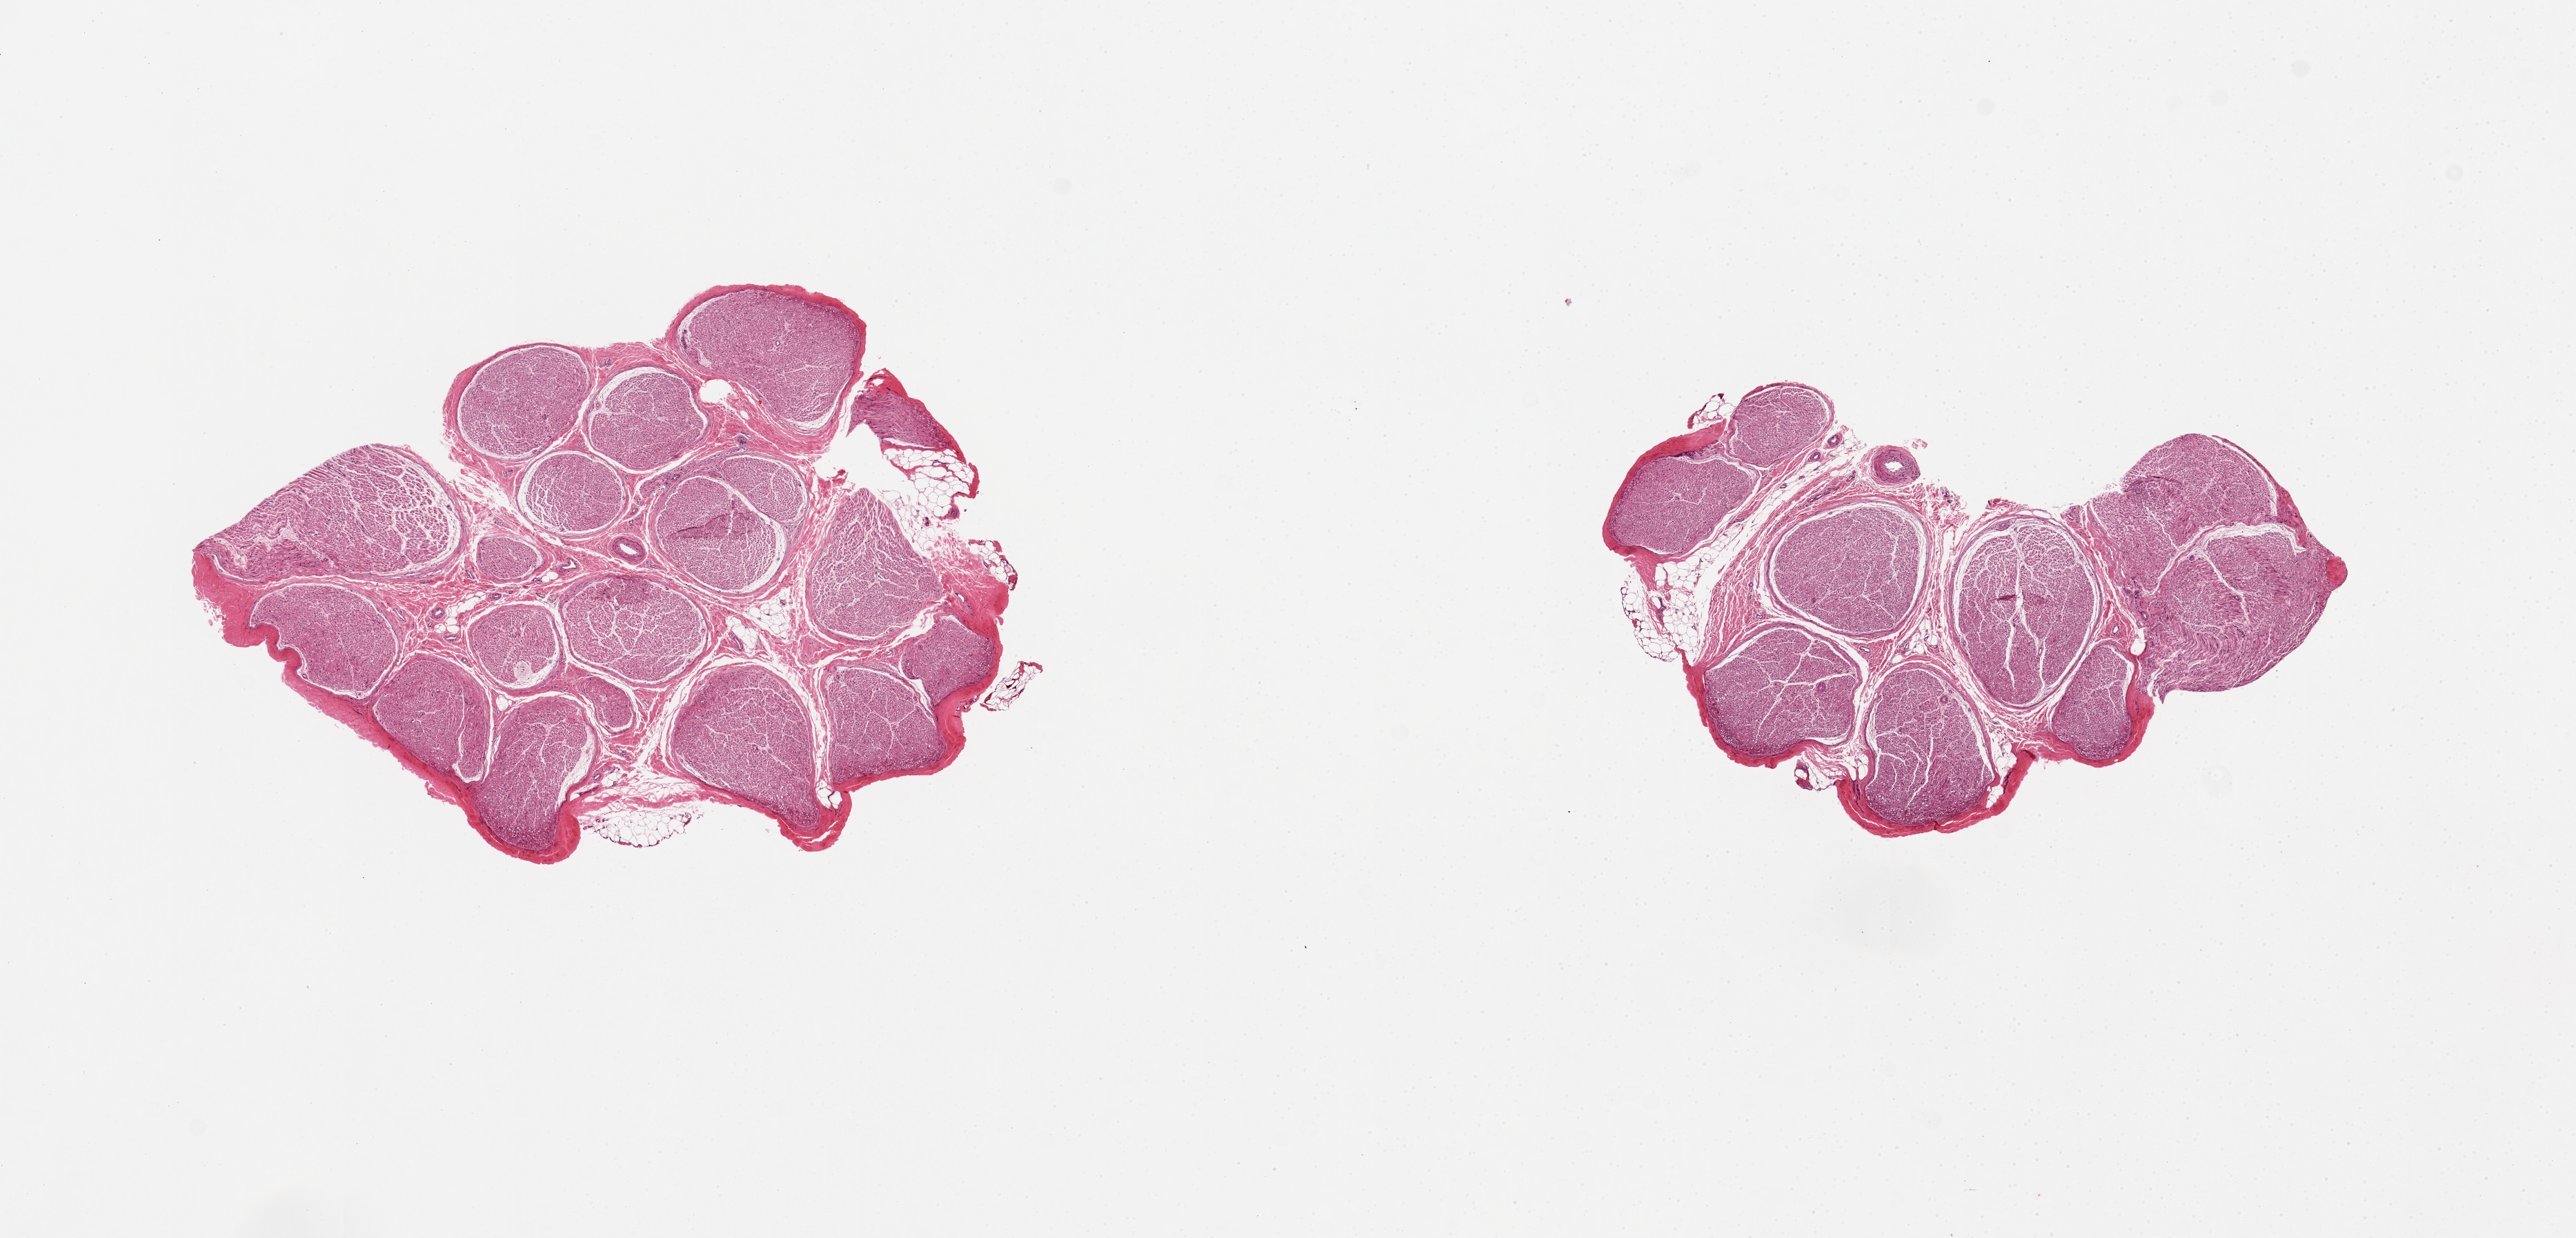
H&E whole-slide image, low-resolution overview of the scanned area, about 14.8 x 7.1 mm (from a 20x scan). PAXgene-fixed paraffin-embedded (PFPE) section. Target tissue: tibial nerve. Donor tissue sample. Male donor.
- pathologist's review note for this sample: 2 pieces, ~3.5mm d